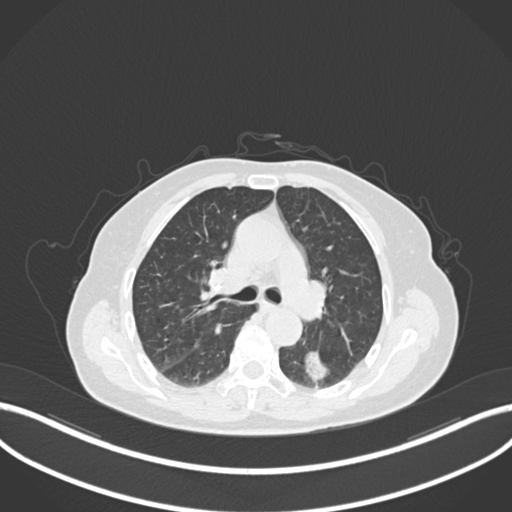
Chest CT, one axial slice. Slice 535 of 727 in the series (ordered by position). Lung window (W 1500 / L -600 HU). 1 mm slice thickness. 512 × 512 image matrix. Female patient, age 70 years. Case-level facts recorded for this patient, not image findings: clinical TNM (as recorded): T1c N0 M0.
Annotated regions visible in this slice (rectangle marked by the reading radiologist):
- lung tumour (recorded histology: adenocarcinoma): bounding box [x1, y1, x2, y2] px = [304, 348, 331, 385]